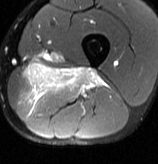
MRI of an extremity soft-tissue mass, one axial slice; position 27 of 70 along the scan axis; T2-weighted fat-saturated; MR volume resampled by the dataset authors to the PET/CT grid (not the native acquisition matrix); 3.27 mm slice thickness; 158 × 164 image matrix, field of view 154 × 160 mm. Male patient. From the clinical record (not read from this slice): histological type: extraskeletal osteosarcoma; grade: high; site of the primary tumour: left adductur.
Structures marked on this image (expert contour drawn on MRI and transferred to this co-registered scan by the dataset authors):
- gross tumour volume (mass): box from (x=22, y=62) to (x=107, y=115) px